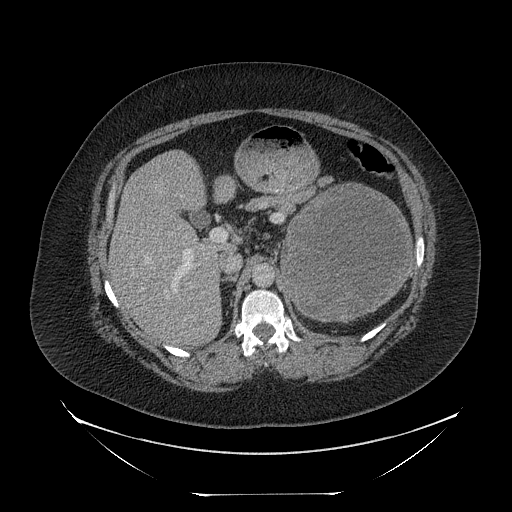
Contrast-enhanced abdominal CT, one axial slice; slice 149 of 205 in the series (ordered by position); reconstruction kernel STANDARD; 120 kVp; soft-tissue window (W 400 / L 40 HU); 512 × 512 image matrix, field of view 500 × 500 mm. Patient: female, 53 years. Case-level facts recorded for this patient, not image findings: diagnosis: adrenocortical carcinoma; tumour side: left adrenal; tumour size at pathology: 17 cm; Ki-67 index: 20 %; stage (as recorded): 3.
Outlined on this slice (semi-automatic segmentation, software-assisted and operator-edited):
- mass: bounding box [x1, y1, x2, y2] px = [283, 185, 411, 320]